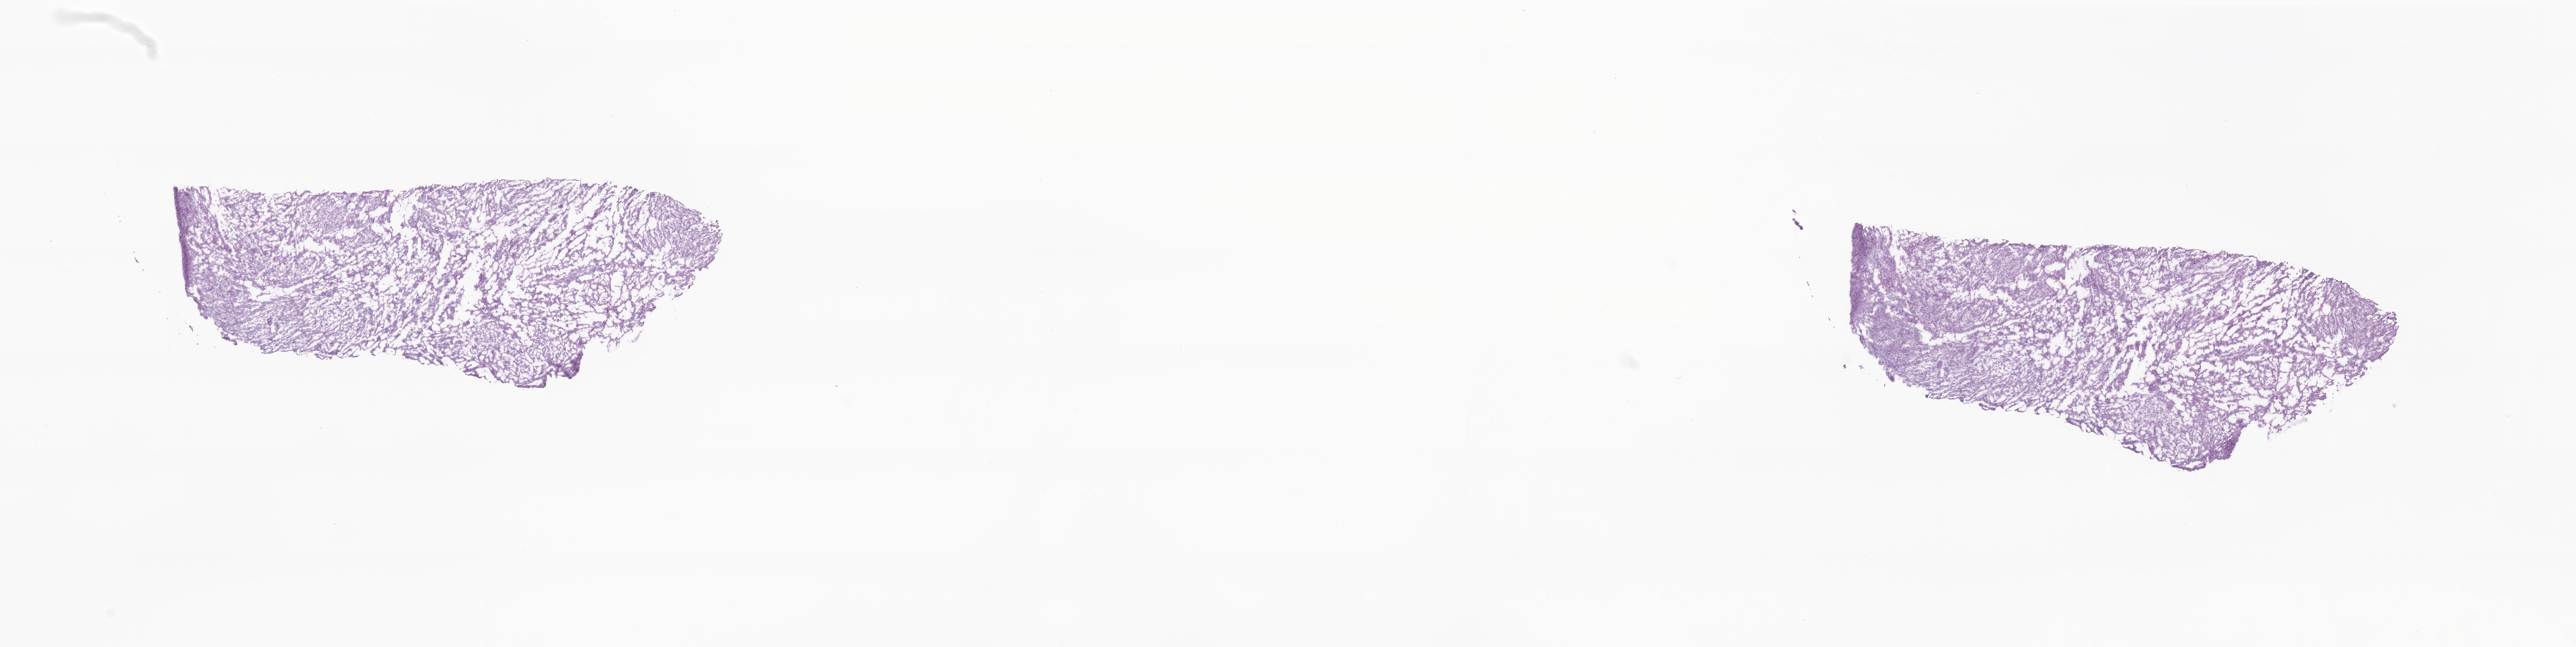
Digitized hematoxylin and eosin (H&E)-stained section — shown as a low-resolution overview of the whole scanned area (about 27.1 x 6.8 mm). Frozen section. Metastatic tumor tissue, resected from abdomen. Female patient; age at initial diagnosis 48 years. Composition of this section per pathologist review: tumor cells 90%, tumor nuclei 90%, stromal cells 10%, necrosis 0%, normal cells 0%. Inflammatory infiltration, as recorded: lymphocyte infiltration 0%, monocyte infiltration 0%, neutrophil infiltration 0%.
Patient diagnosis (primary): Leiomyosarcoma, NOS.